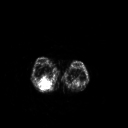
FDG PET of an extremity soft-tissue mass (from a PET/CT study), one axial slice; slice 168 of 267 in the series (ordered by position); 128 × 128 image matrix. Female patient, age 62 years. Case-level facts recorded for this patient, not image findings: histological type: liposarcoma; site of the primary tumour: right thigh.
Outlined on this slice (expert contour drawn on MRI and transferred to this co-registered scan by the dataset authors):
- gross tumour volume (mass): bounding box [x1, y1, x2, y2] px = [38, 78, 52, 90]